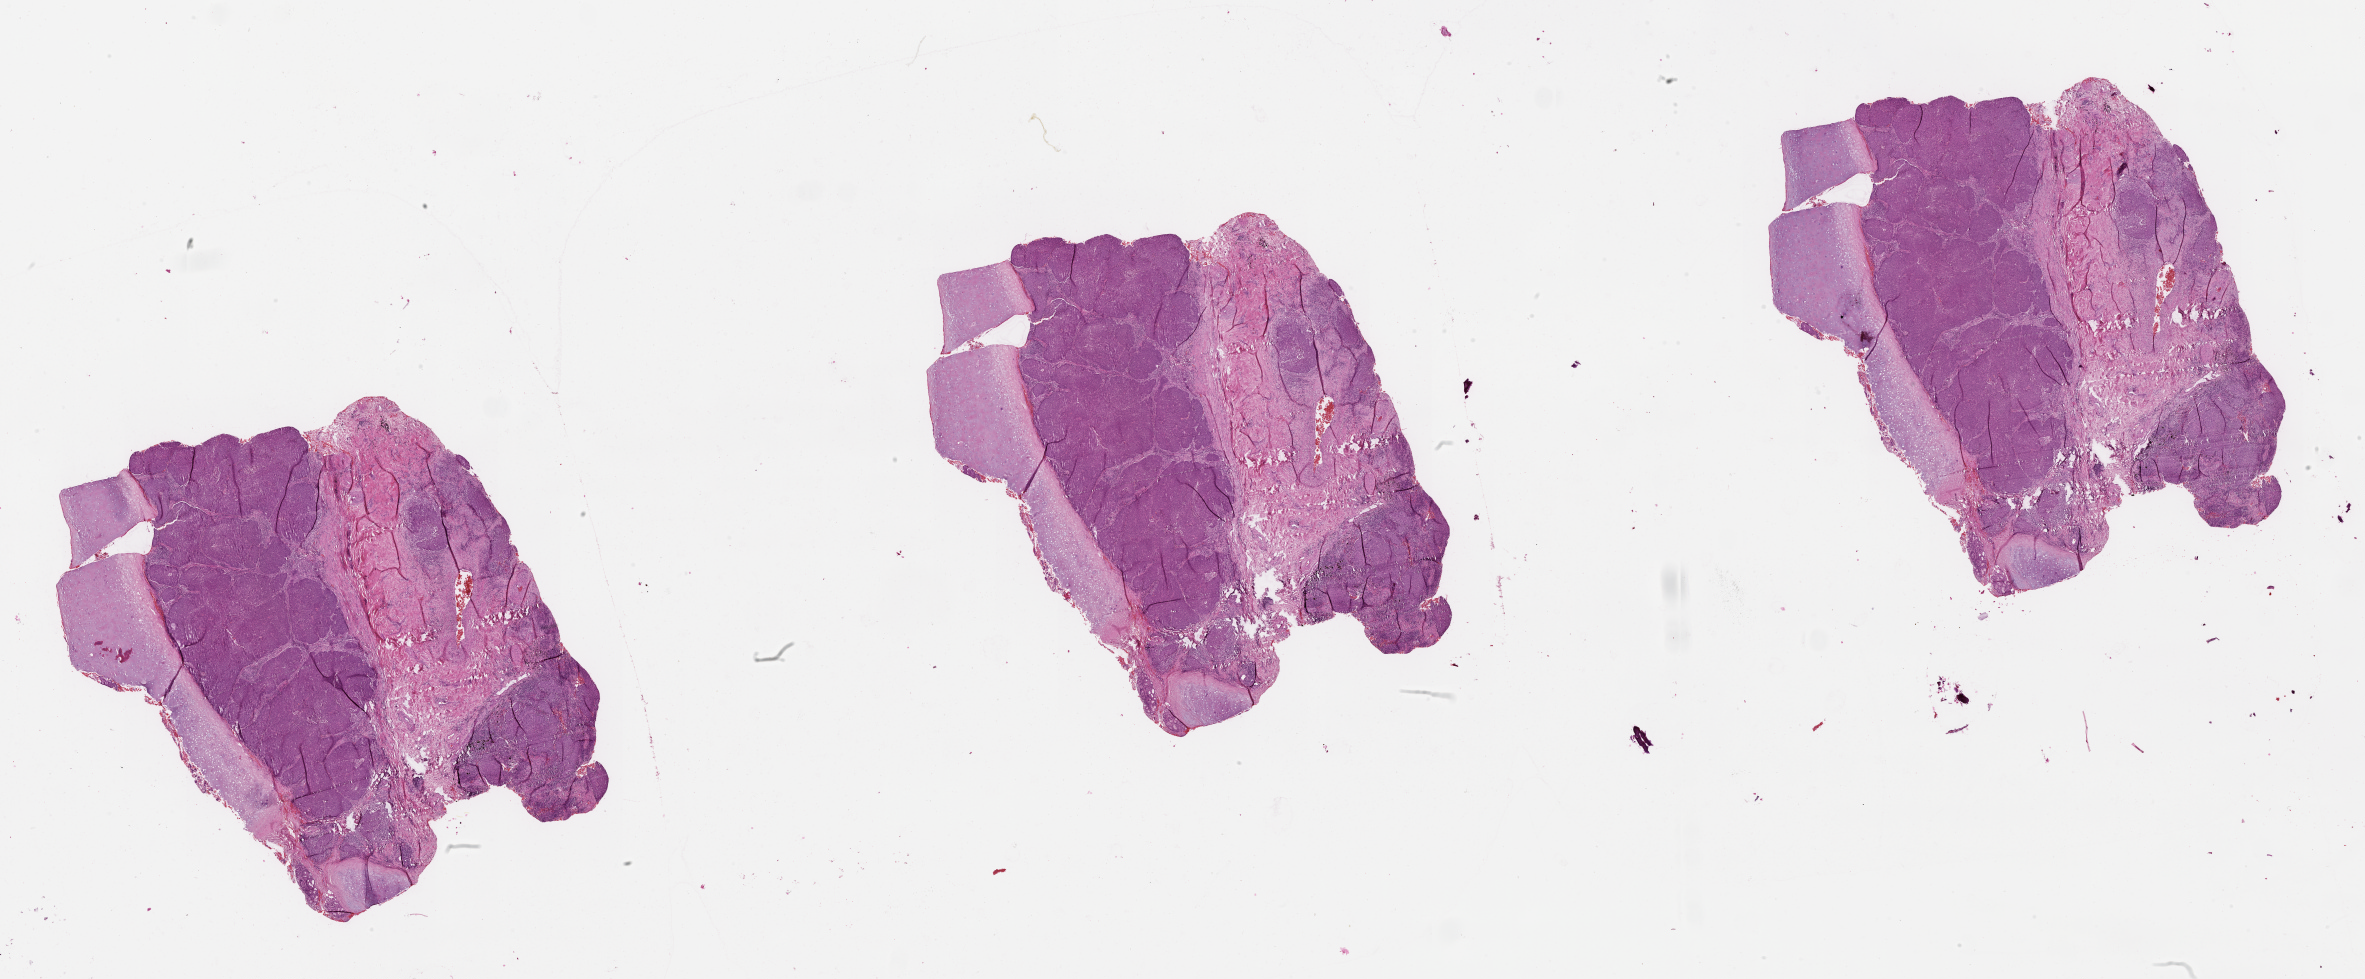
Hematoxylin and eosin (H&E) stained whole-slide image, low-resolution overview of the scanned area, about 38.1 x 15.8 mm (slide scanned at 20x); tumour tissue sample, lung. Patient: male, age 71 years.
Patient diagnosis (cohort enrolment): squamous cell carcinoma (lung).